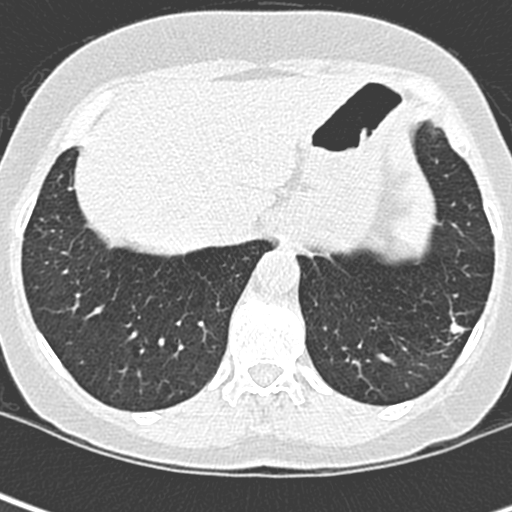
Low-dose screening chest CT, one axial slice. Slice 59 of 252 in the series (ordered by position). 120 kVp. Lung window (W 1500 / L -600 HU). 1.3 mm slice thickness. 512 × 512 image matrix, field of view 271 × 271 mm.
Annotated regions visible in this slice (outlined manually by an expert reader):
- lesion 1 (tumor, lower lobe of left lung): bounding box (x1, y1, x2, y2) in pixels: (450, 321, 467, 337)